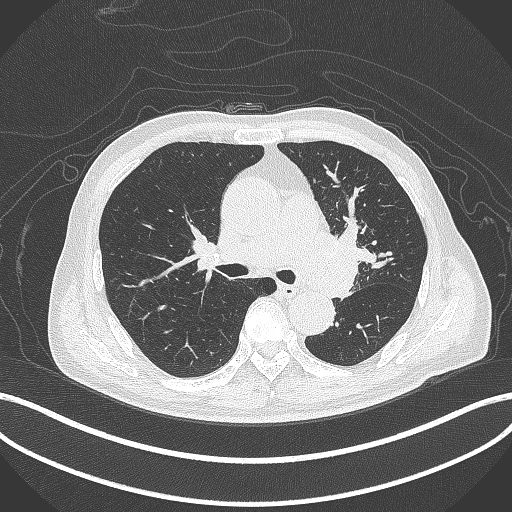
Chest CT, one axial slice; slice 266 of 417 in the series (ordered by position); 120 kVp; lung window (W 1500 / L -600 HU); 1 mm slice thickness; 512 × 512 image matrix. Patient: male, 77 years. Case-level facts recorded for this patient, not image findings: clinical TNM (as recorded): T3 N1 M0.
Structures marked on this image (rectangle marked by the reading radiologist):
- lung tumour (recorded histology: adenocarcinoma): bounding box (x1, y1, x2, y2) in pixels: (305, 225, 371, 303)